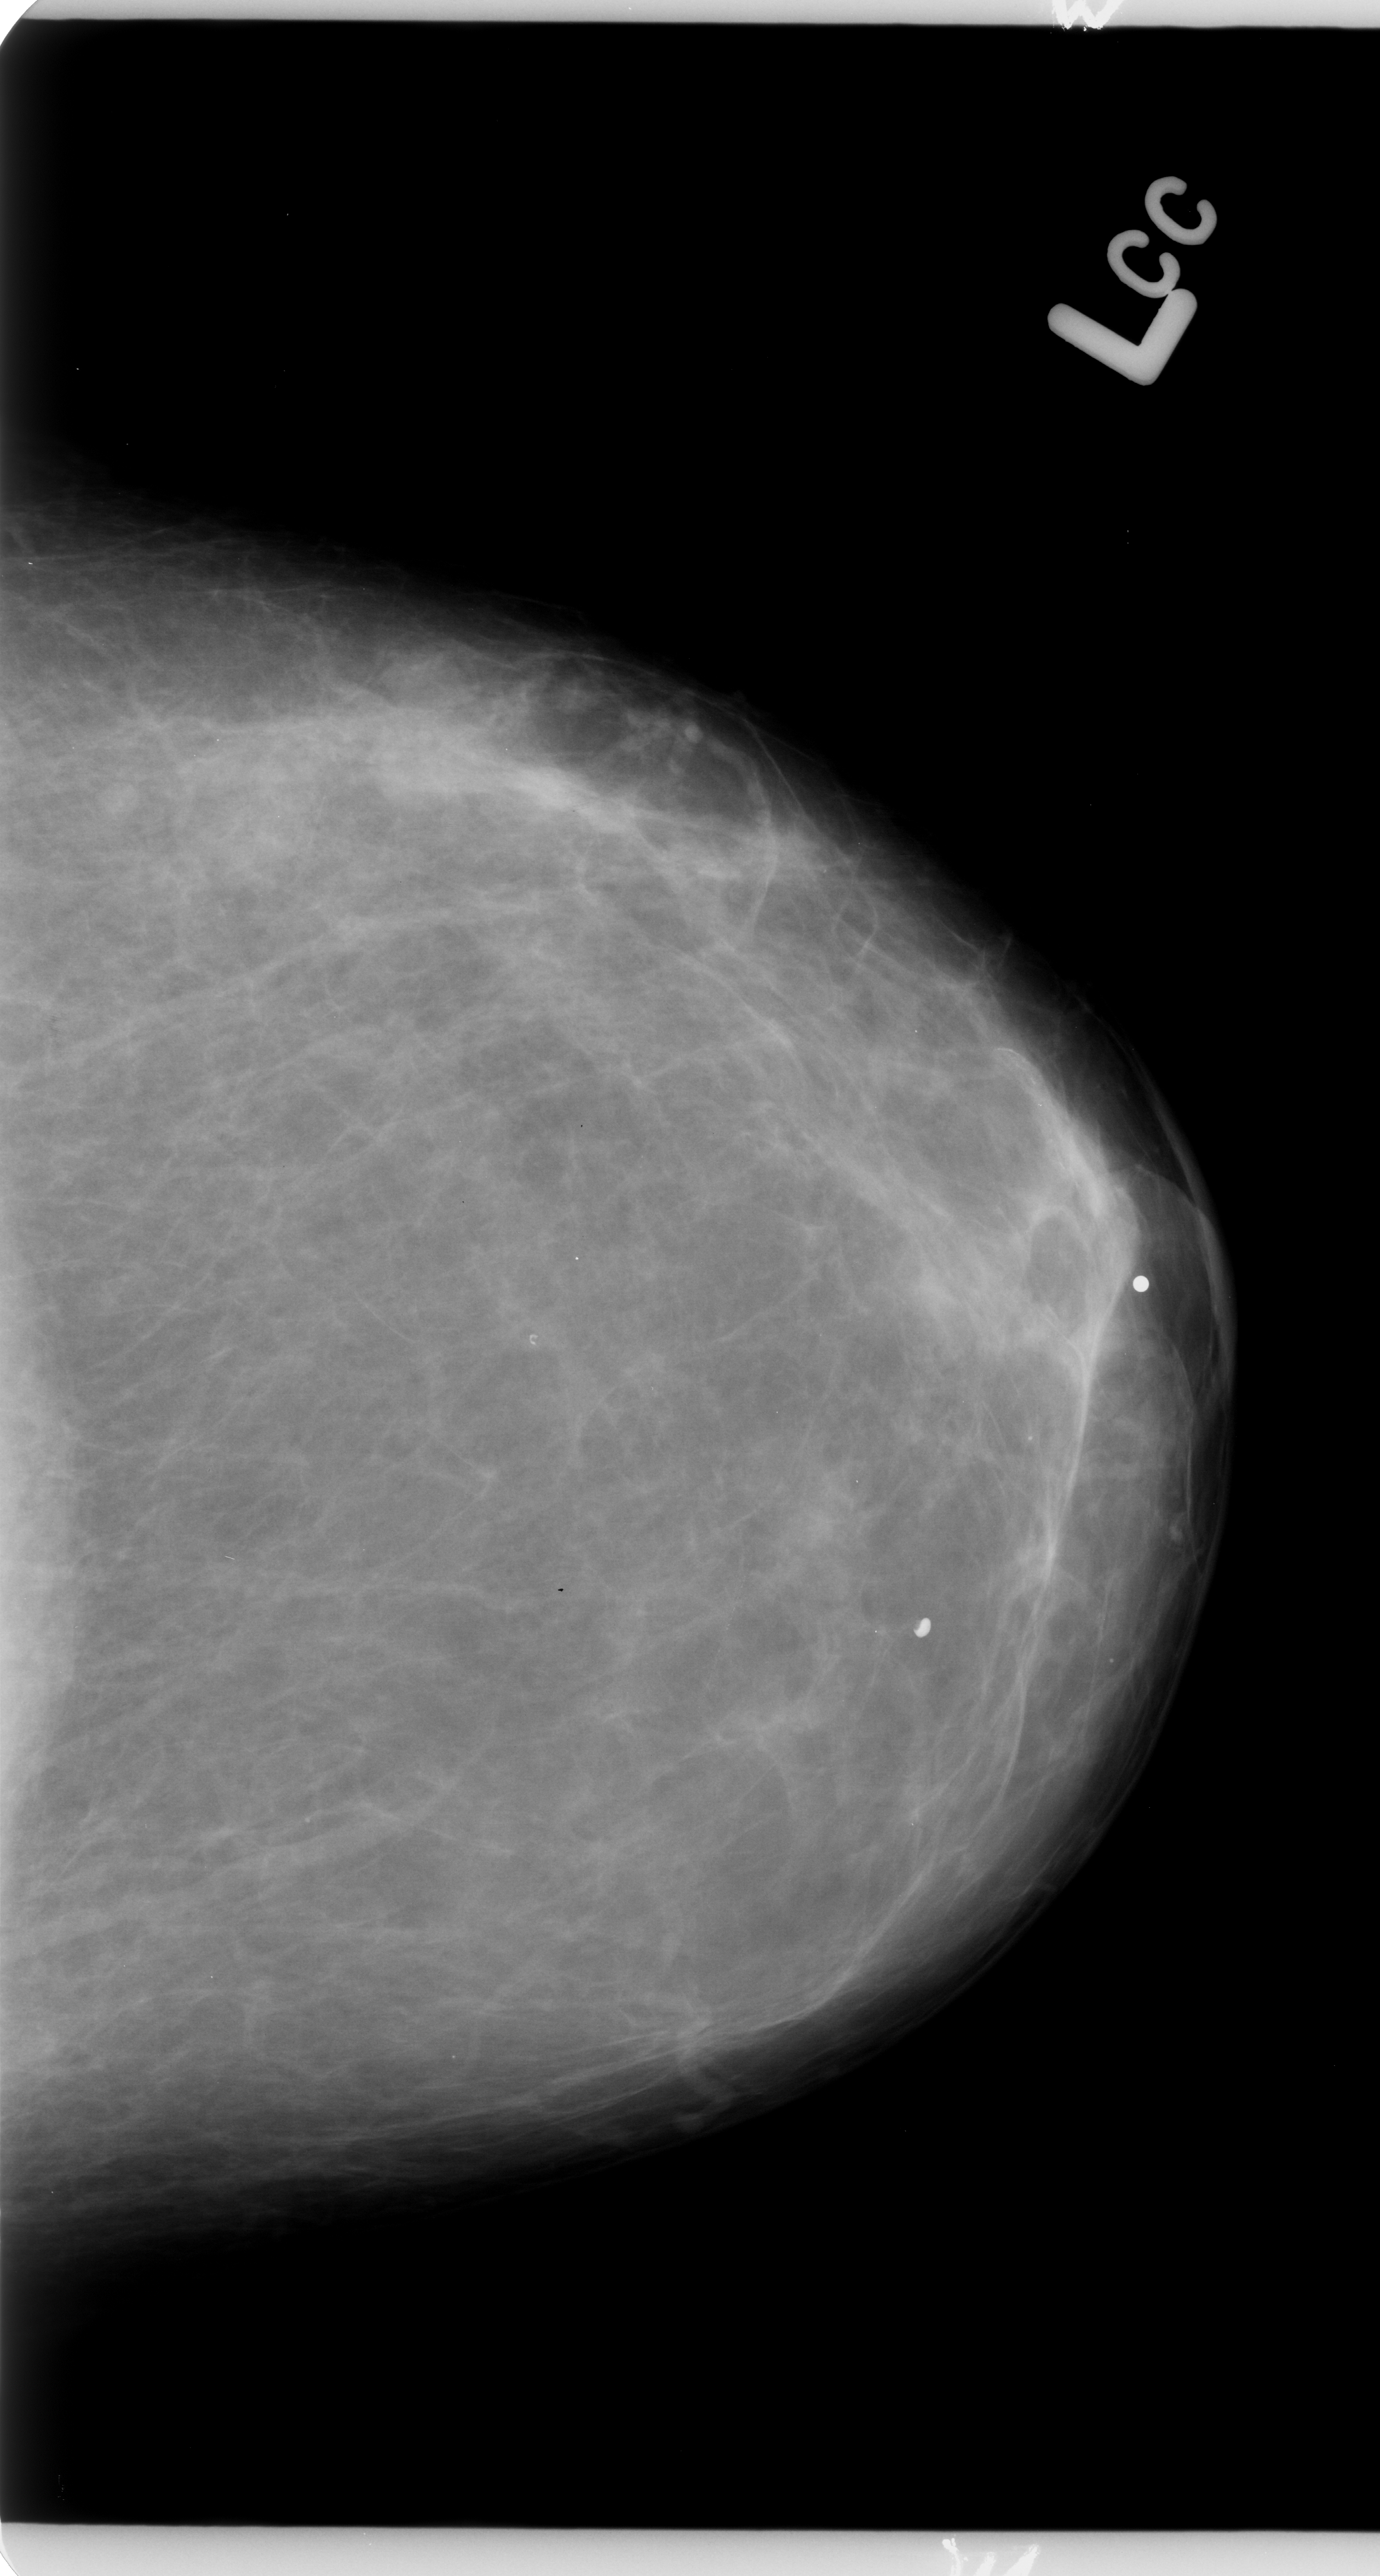
Mammogram (digitized film). Left breast. Craniocaudal (CC) view. BI-RADS breast density category 2 (scale 1–4). 1380 × 2576 image matrix.
Expert-marked regions of interest on this image (one box per marked abnormality):
- mass, shape irregular, margins ill defined; BI-RADS assessment category 3; subtlety rating 3 on a 1 (subtle) to 5 (obvious) scale; pathology result (as recorded, not read from the image): benign: bounding box (x1, y1, x2, y2) in pixels: (364, 667, 572, 836)